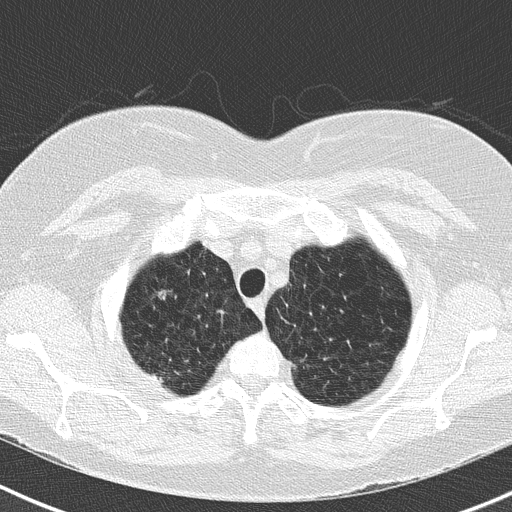
Axial slice from a low-dose chest CT screening exam, second annual screen, lung window (W 1500 / L -600 HU), 2 mm slice thickness, lung (sharp) reconstruction kernel (B50f). Female, age 73 years at enrolment. Former smoker at enrolment.
- Expert reader's lesion annotation, bounding box <134,273,190,318> (left, top, right, bottom; pixels).
- The screening reader recorded 2 non-calcified nodules or masses ≥4 mm on this exam (right upper lobe, right upper lobe); which of them this box marks is not recorded.
- Official screen result: positive, no significant change: stable abnormalities potentially related to lung cancer, unchanged since the prior screening exam.
- Later outcome: lung cancer diagnosed 250 days after this screen — adenocarcinoma, NOS, right upper lobe, moderately differentiated (G2), stage IB (AJCC 6th edition), 15 mm at pathology.